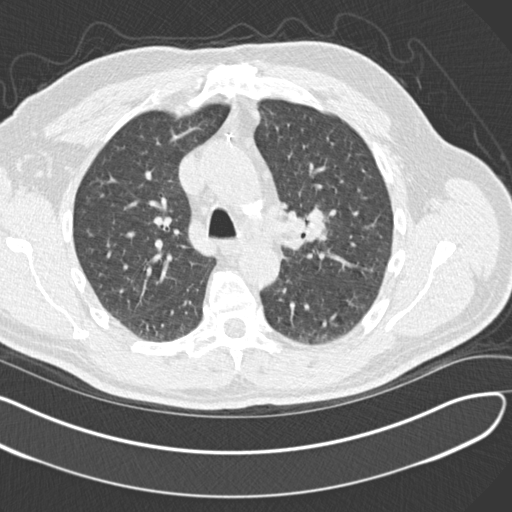
Low-dose screening chest CT, axial slice, second screening round (one year after baseline), lung window (W 1500 / L -600 HU), 120 kVp. Male participant, aged 65 years at enrolment. Former smoker at enrolment.
- Lesion marked by an expert reader, bounding box [x1, y1, x2, y2] px = [287, 196, 347, 259].
- The screening reader recorded 4 non-calcified nodules or masses ≥4 mm on this exam (left upper lobe, left upper lobe, left lower lobe, right middle lobe); which of them this box marks is not recorded.
- Lung cancer was diagnosed 577 days after this screen (after the third annual screen): acinar cell carcinoma, left upper lobe, stage IA (AJCC 6th edition), 25 mm at pathology.